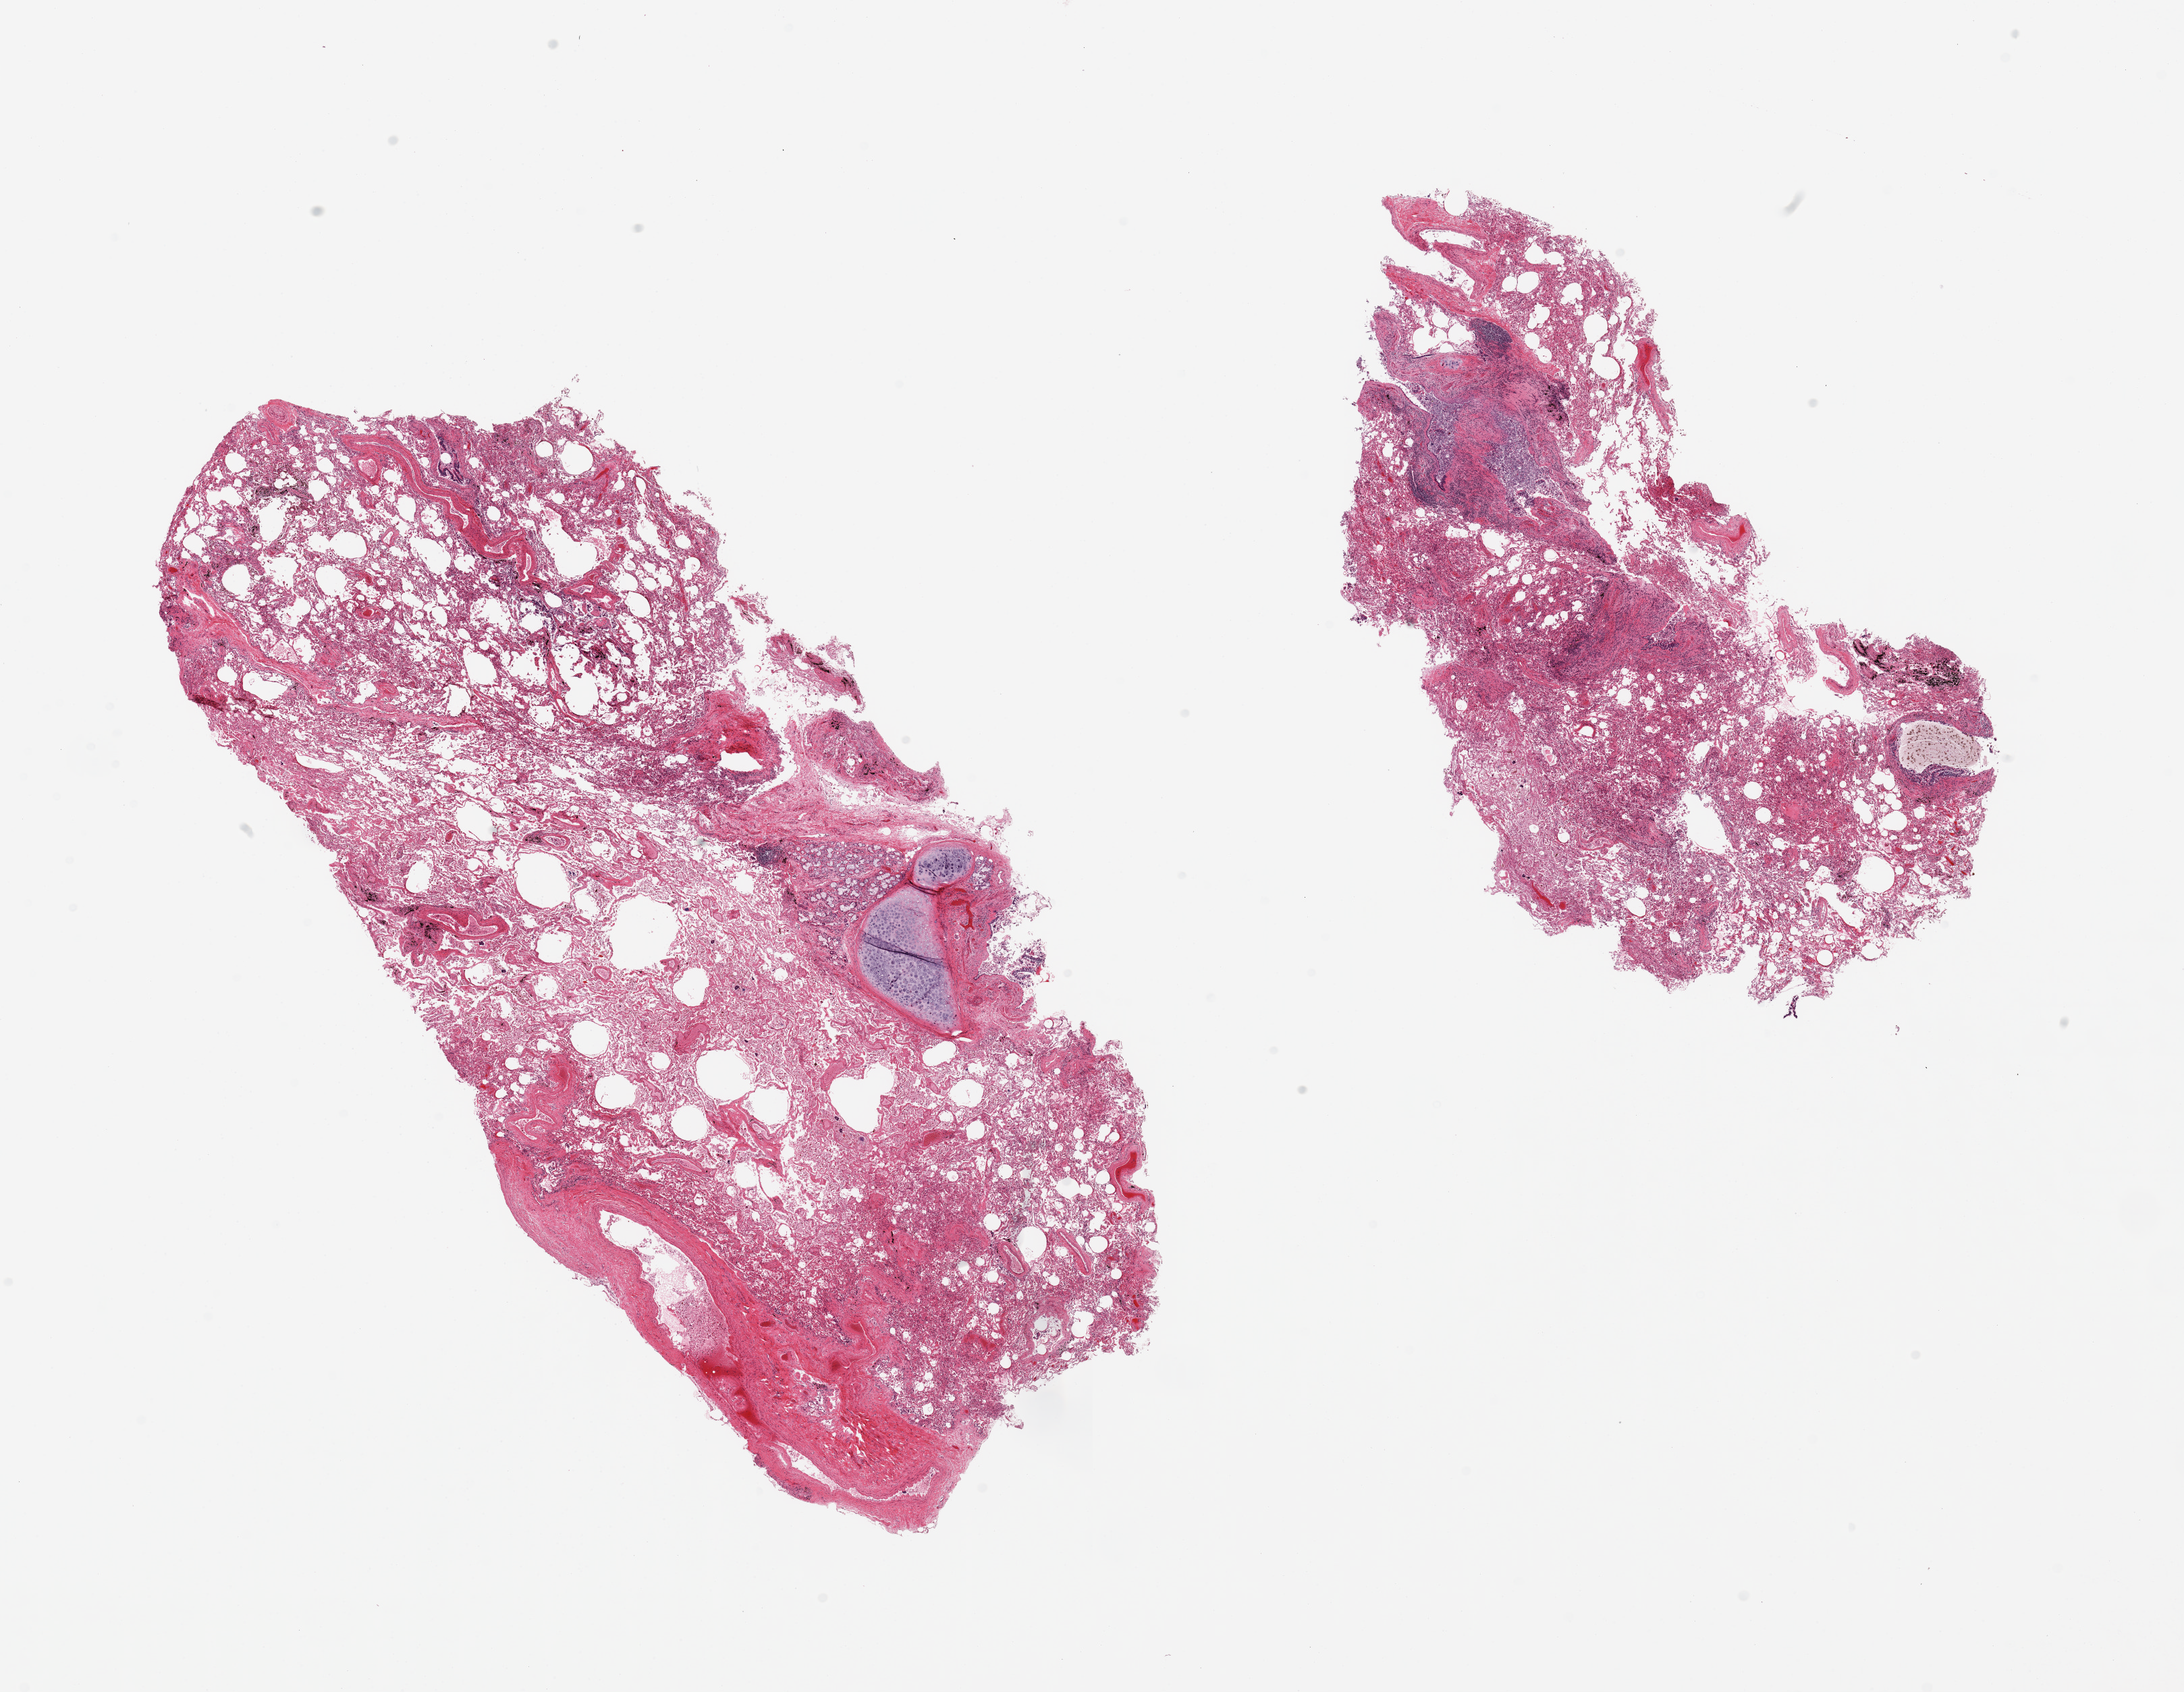
Haematoxylin and eosin whole-slide image — shown as a low-resolution overview of the whole scanned area (about 25.6 x 19.8 mm), PAXgene-fixed paraffin-embedded (PFPE) section, target tissue: lung, tissue donor sample. Donor sex: male.
- reviewer comment on this tissue sample: 2 pieces; hemosiderin-laden macrophages, anthracotic pigment, several large vessels and foci of cartilage and submucosal glands, focal bronchopneumonia